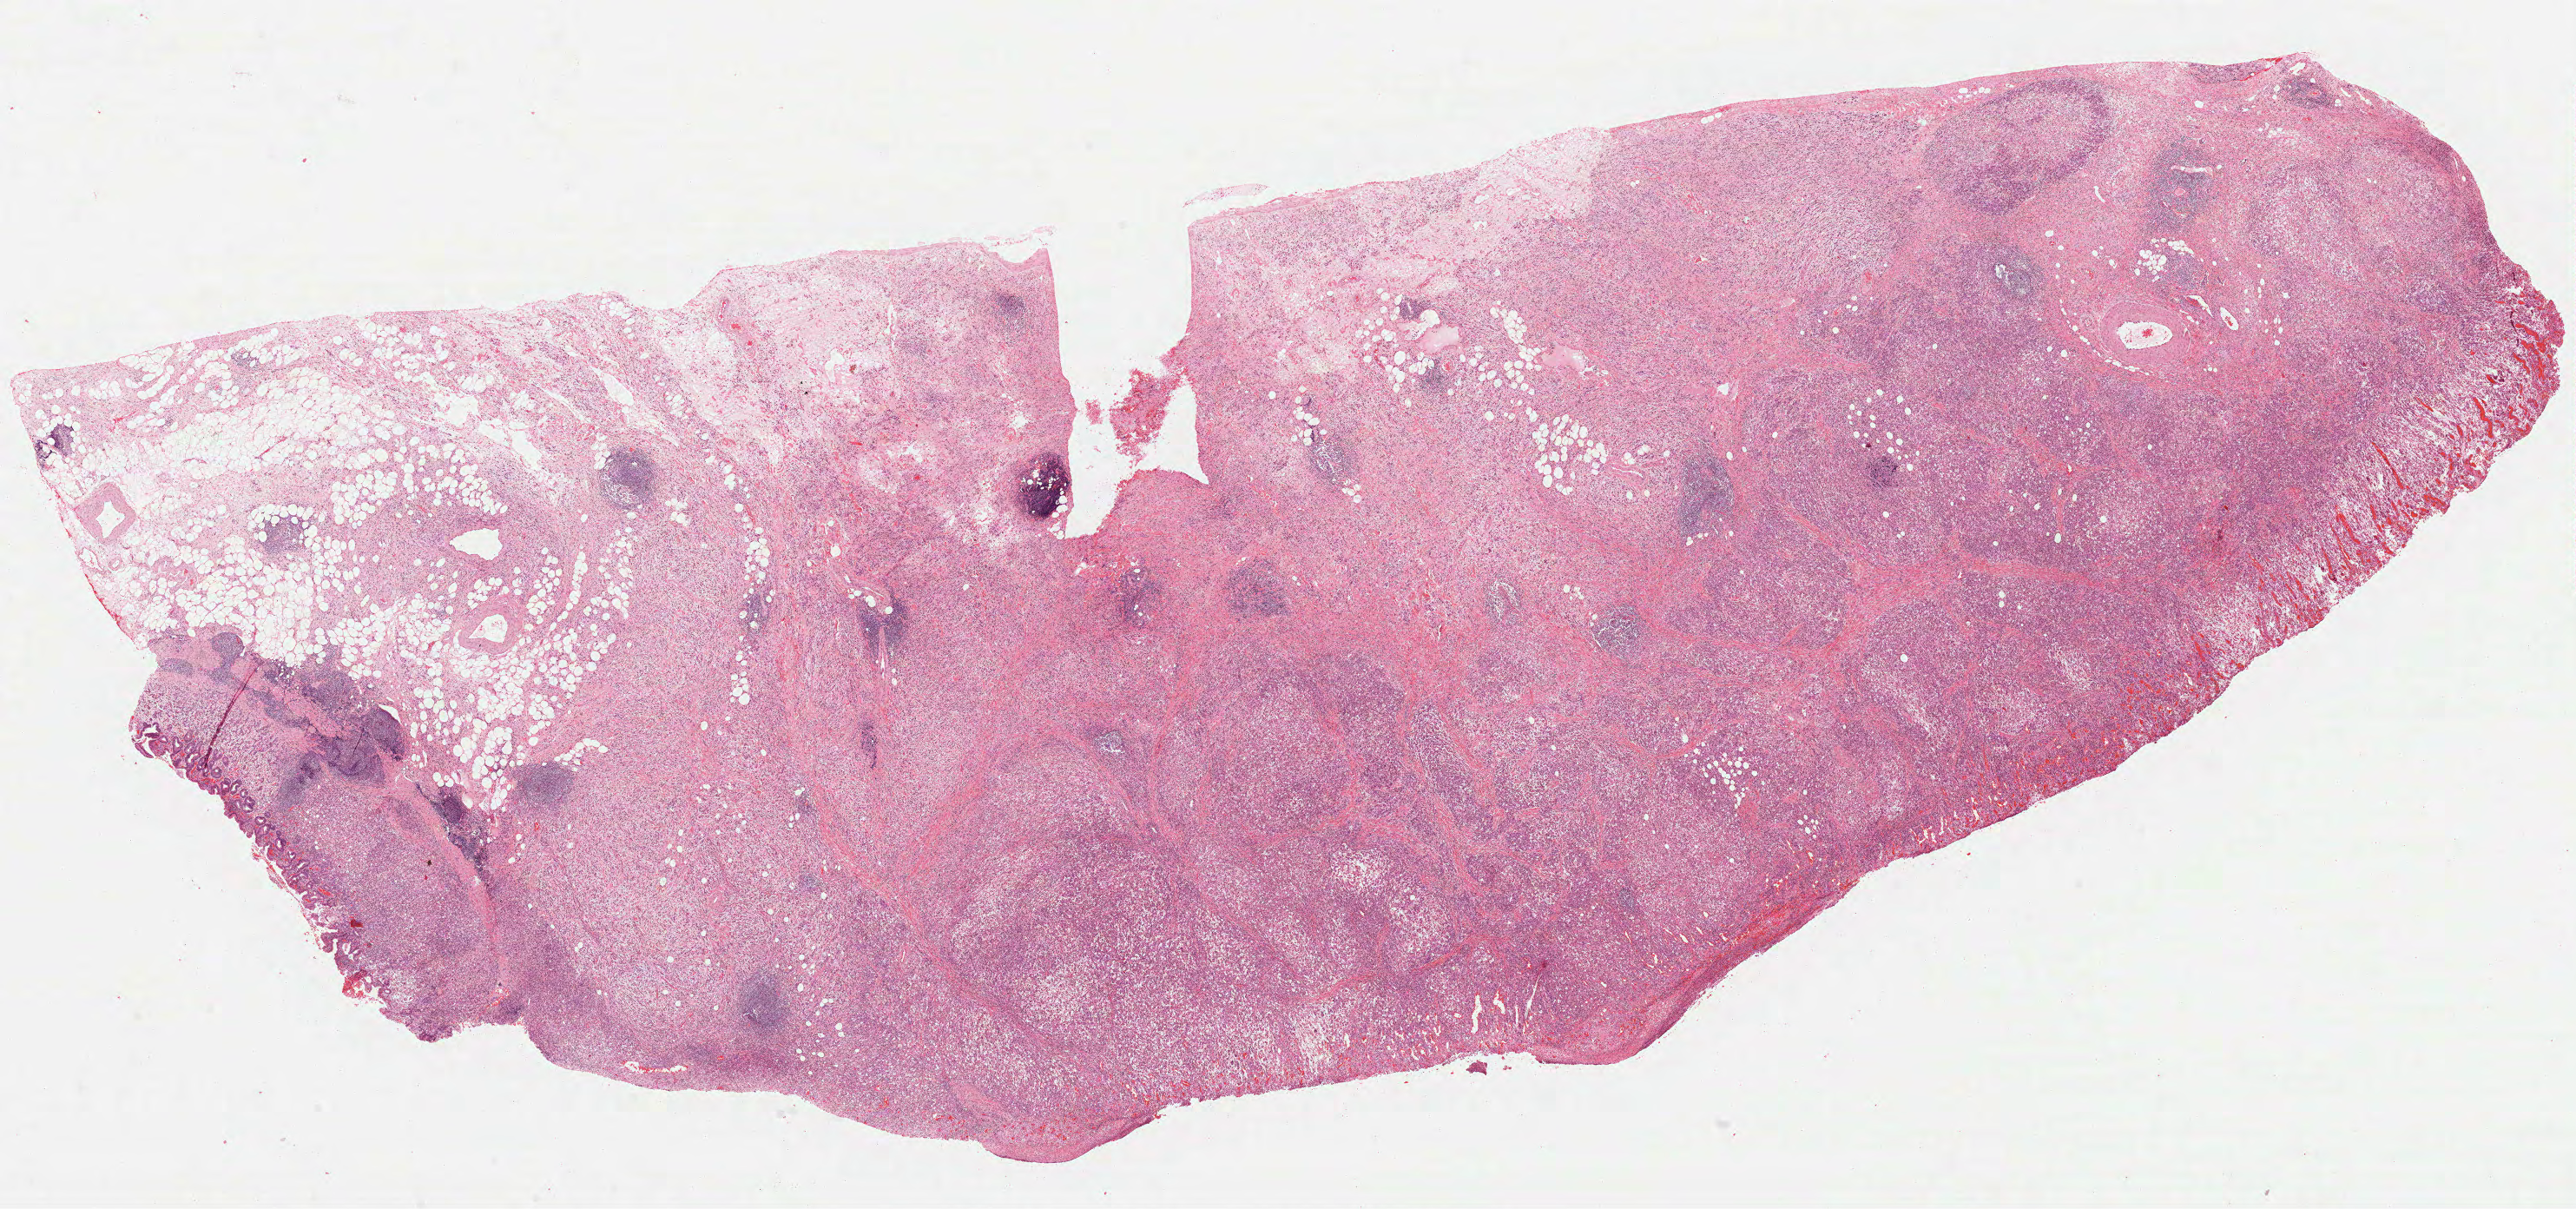
Whole-slide histology image, H&E-stained, whole scanned area (about 23.9 x 11.2 mm) shown as a low-resolution overview. FFPE section. Primary tumour sample from the stomach. Male, age 54 years at initial diagnosis. Histologic grade: G3 (poorly differentiated).
AJCC pathologic stage: IIA. Pathologic diagnosis: Adenocarcinoma, NOS. Lymph nodes positive (case pathology): 1 of 2 examined.